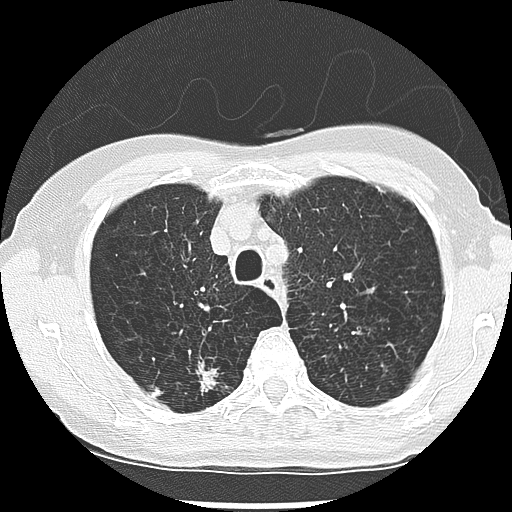
Low-dose screening chest CT, one axial slice; position 213 of 265 along the scan axis; 120 kVp; lung window (W 1500 / L -600 HU); 512 × 512 image matrix, field of view 300 × 300 mm.
Outlined on this slice (outlined manually by an expert reader):
- lesion 1 (nodule, upper lobe of right lung): box from (x=198, y=364) to (x=218, y=393) px